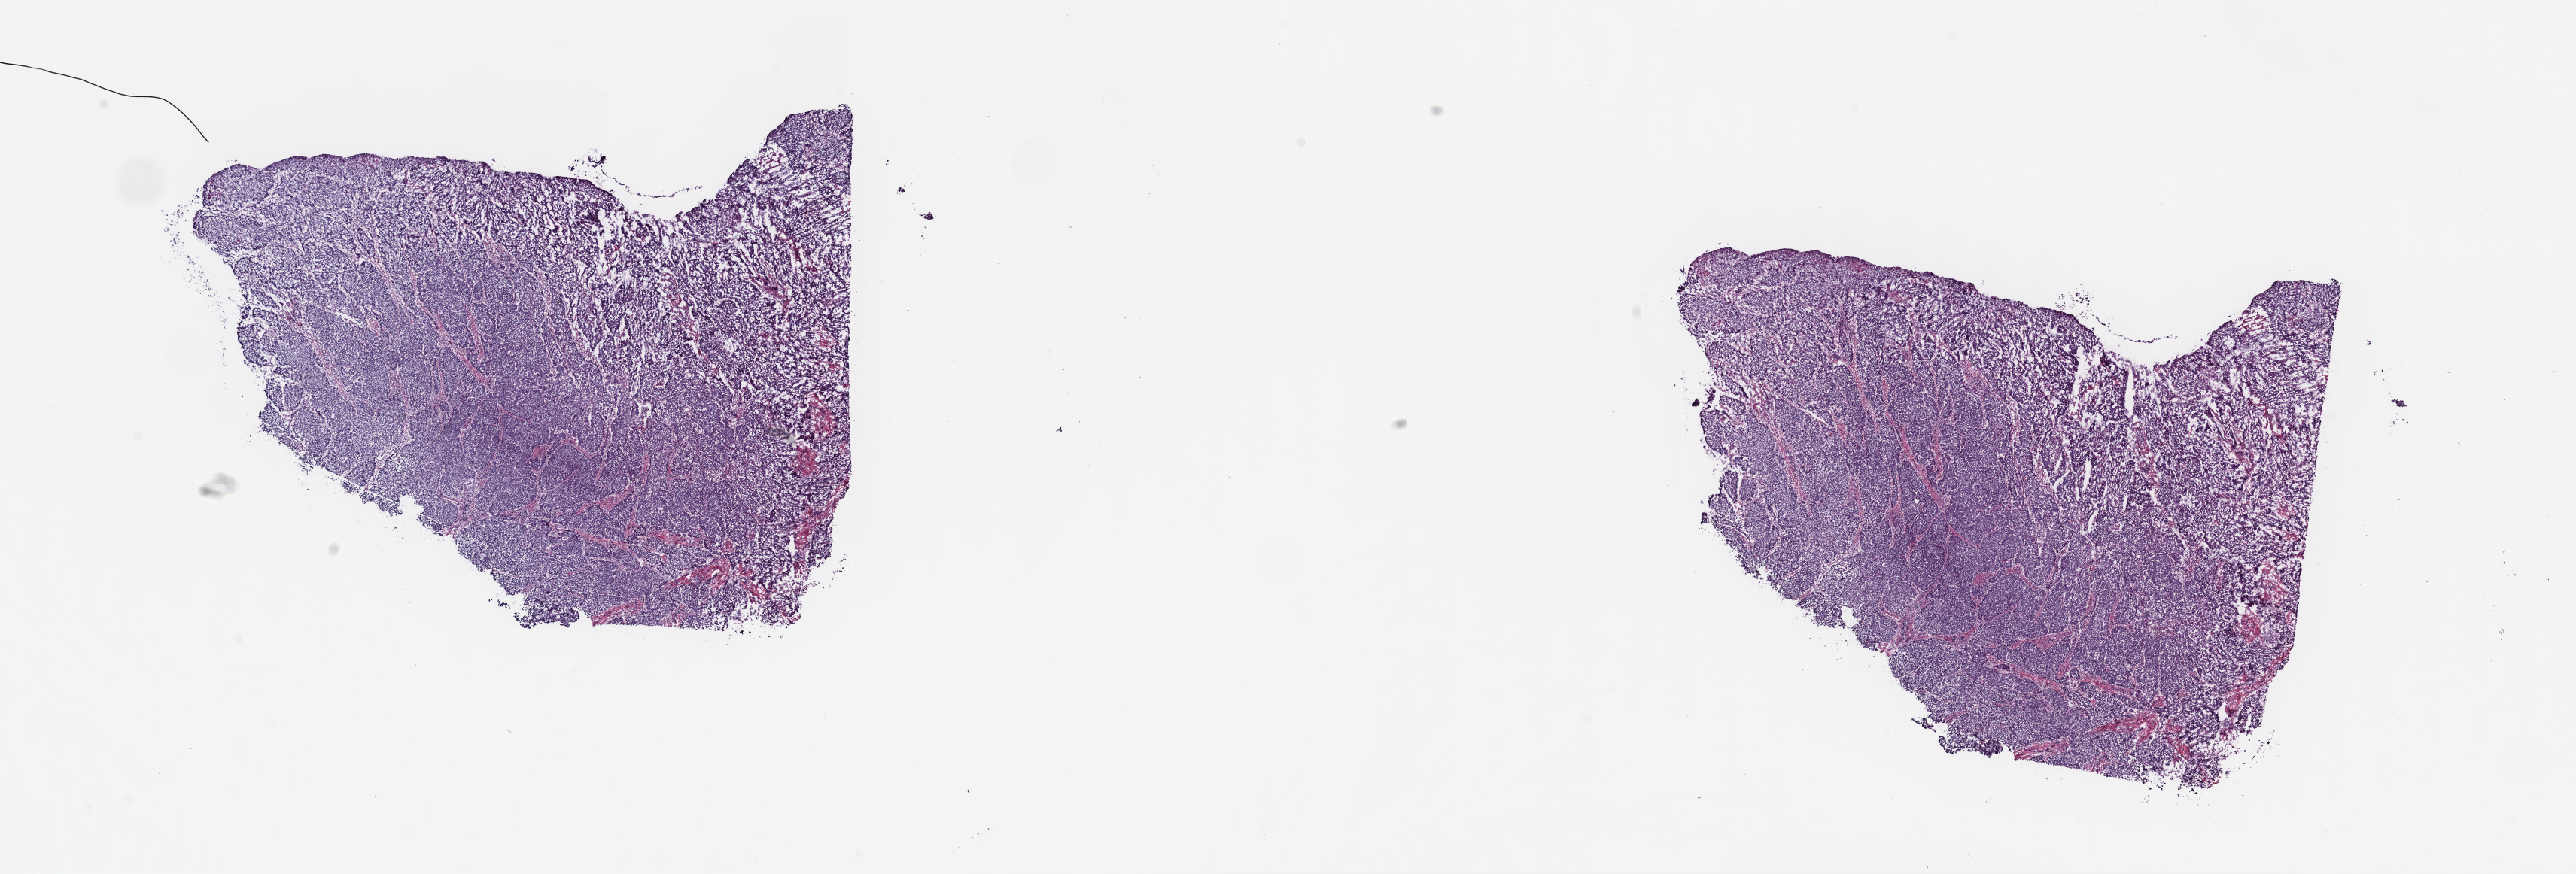
Digitized H&E tissue section (whole slide), whole scanned area (about 27.7 x 9.4 mm, from a 40x scan) shown as a low-resolution overview, frozen section, sample: primary tumour, esophagus. Female, age 67 years at initial diagnosis. Histologic grade: G3 (poorly differentiated). Slide review estimates, as recorded: tumour cells 81%, tumour nuclei 88%, normal cells 0%, stromal cells 15%, necrosis 4%. Inflammatory infiltration, as recorded: lymphocyte infiltration 8%, monocyte infiltration 2%, neutrophil infiltration 2%.
TNM: T2 N0 M0. AJCC pathologic stage: IIA (6th edition). Diagnosis: Squamous cell carcinoma, NOS.